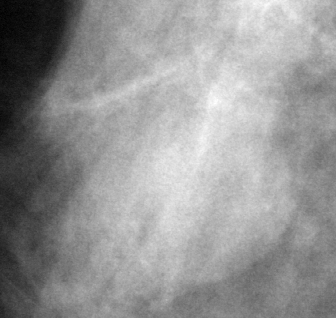
Region of interest cut from a scanned film mammogram (one marked finding); right breast; MLO view; BI-RADS breast density category 2 (scale 1–4).
Mass, shape oval, margins circumscribed; BI-RADS assessment category 3; subtlety rating 4 on a 1 (subtle) to 5 (obvious) scale; pathology (as recorded): benign.